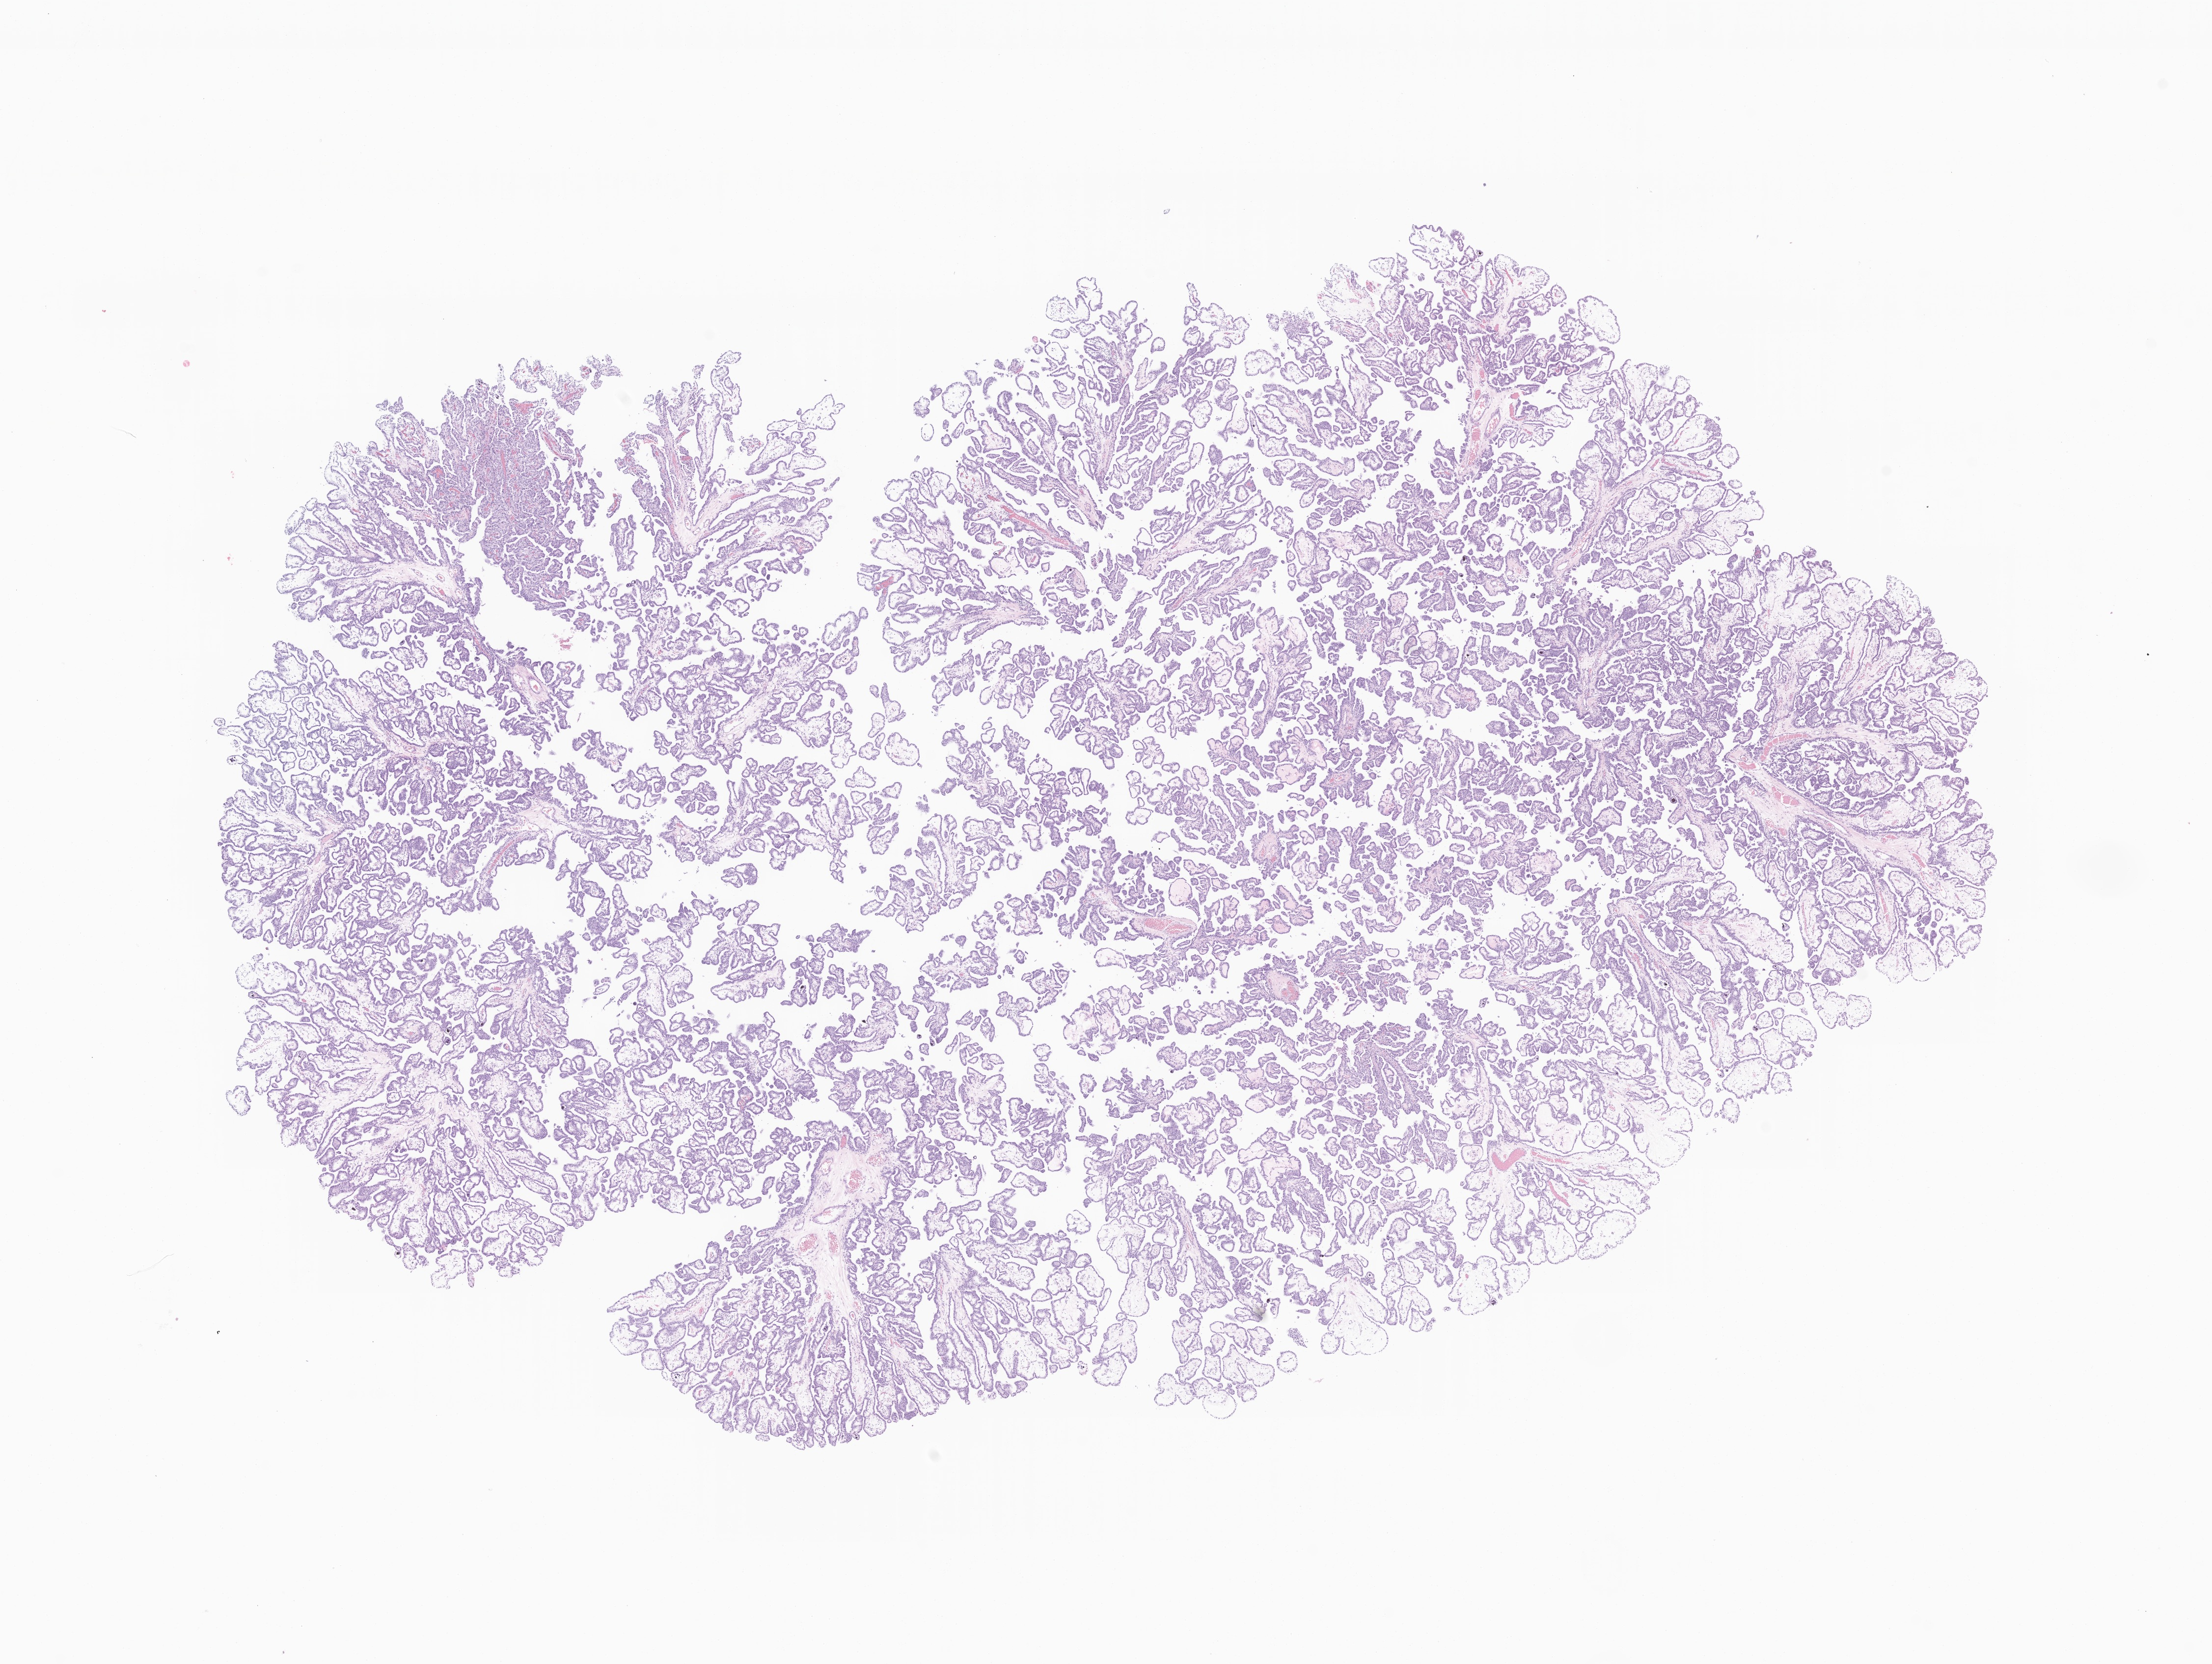
H&E whole-slide image of tumor tissue from the brain, whole scanned area (about 19.0 x 14.3 mm) shown as a low-resolution overview, formalin-fixed, paraffin-embedded (FFPE) tissue. Female patient, age 259 months (21 years 7 months).
Recorded diagnosis: Atypical choroid plexus papilloma.